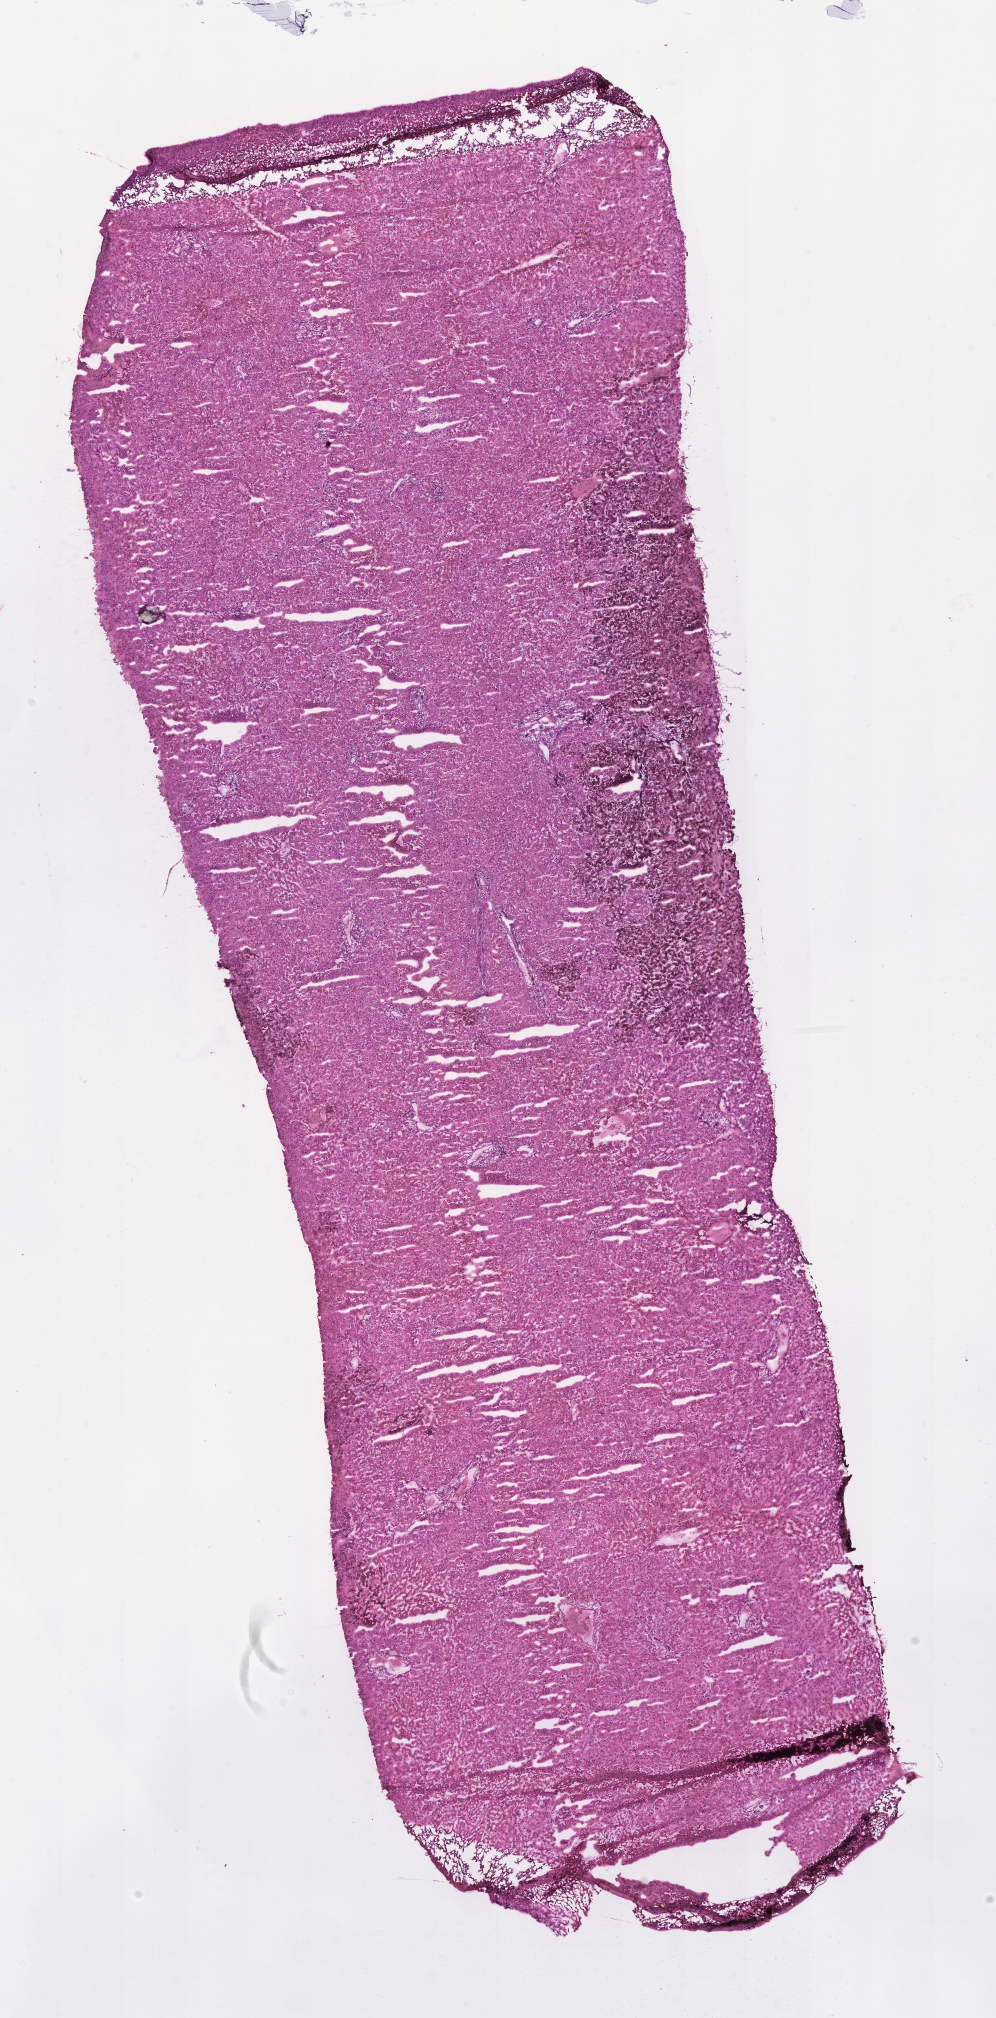
Digitized hematoxylin and eosin (H&E)-stained section — a low-resolution overview of the entire scanned area, about 8.1 x 16.3 mm; cryosection; specimen: non-tumor (normal tissue) sample from a patient with adenocarcinoma, NOS; anatomic site: colon. Male patient; age at initial diagnosis 84 years. Slide review estimates, as recorded: tumor cells 0%, tumor nuclei 0%, stromal cells 0%, necrosis 0%, normal cells 100%. Infiltration values recorded for this section: lymphocyte infiltration 5%, monocyte infiltration 0%, neutrophil infiltration 0%.
This section: non-tumor tissue sample; the patient's diagnosis is given above. Section: top of the tissue portion.